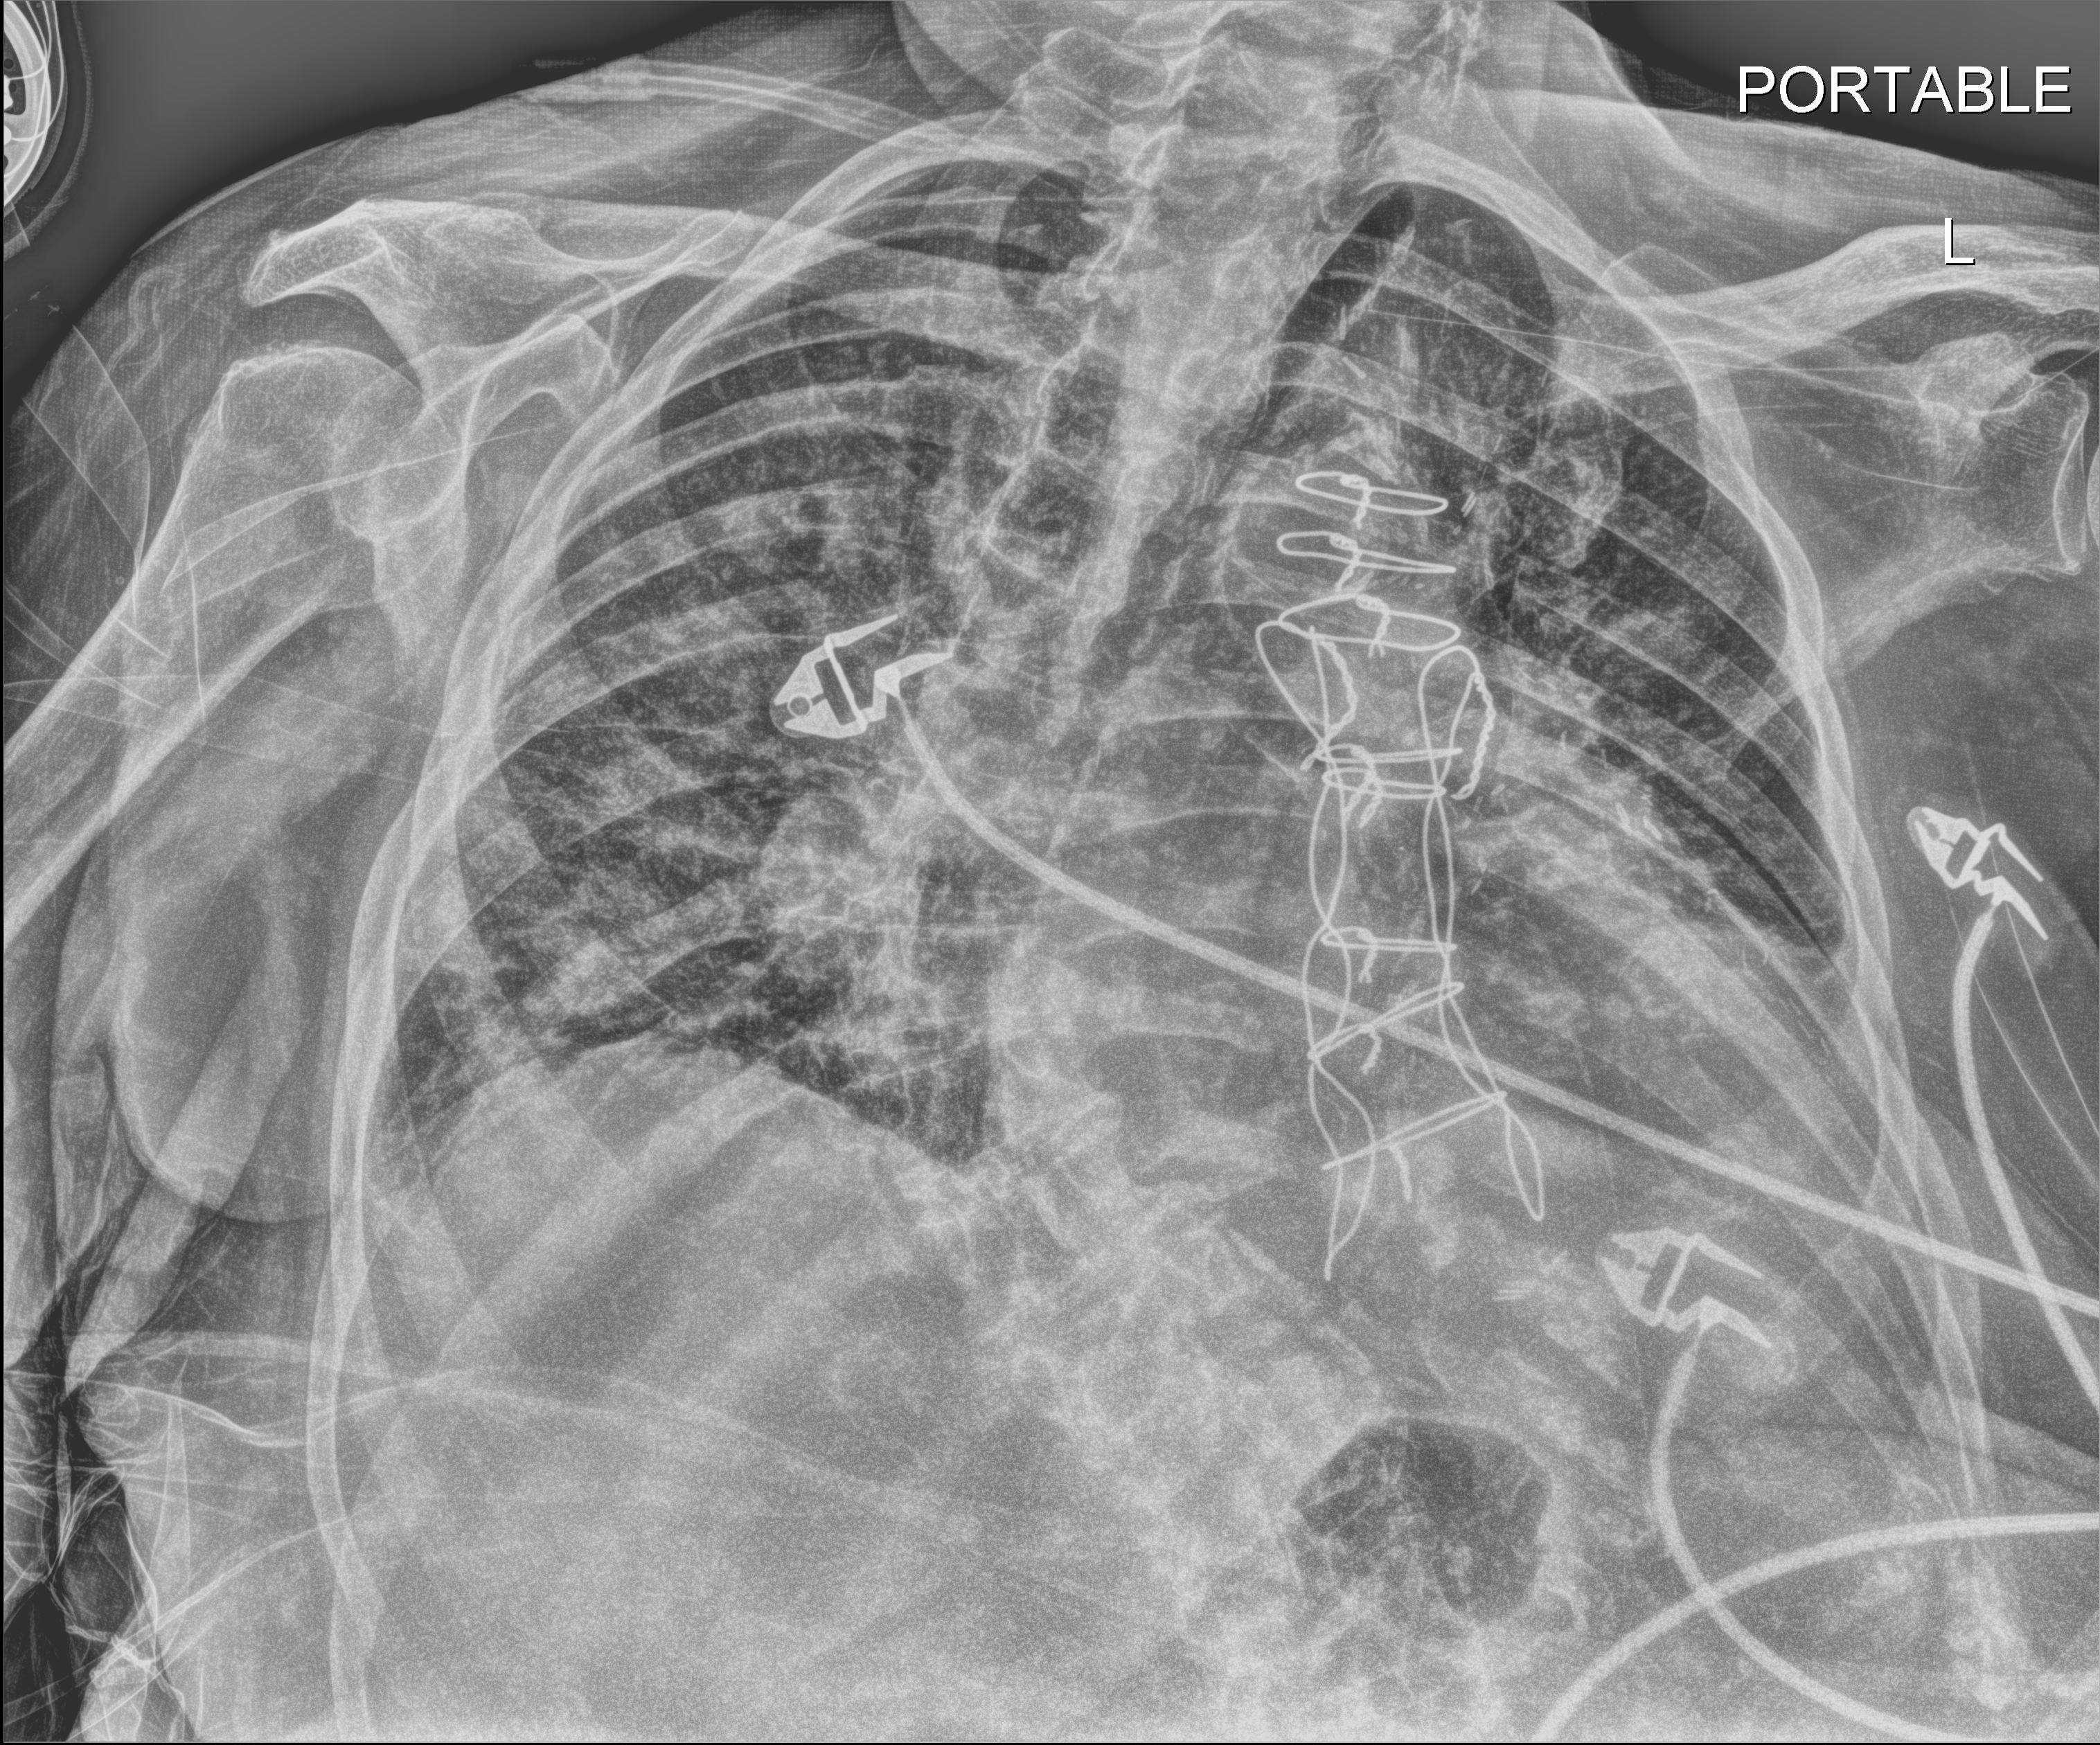
Chest X-ray (portable); anteroposterior (AP) projection. Patient hospitalised with COVID-19; female, aged 75–90 years.
Hospital-stay facts (about this admission, not read from this image; timing relative to this image not recorded): mechanically ventilated during this hospital stay: no.